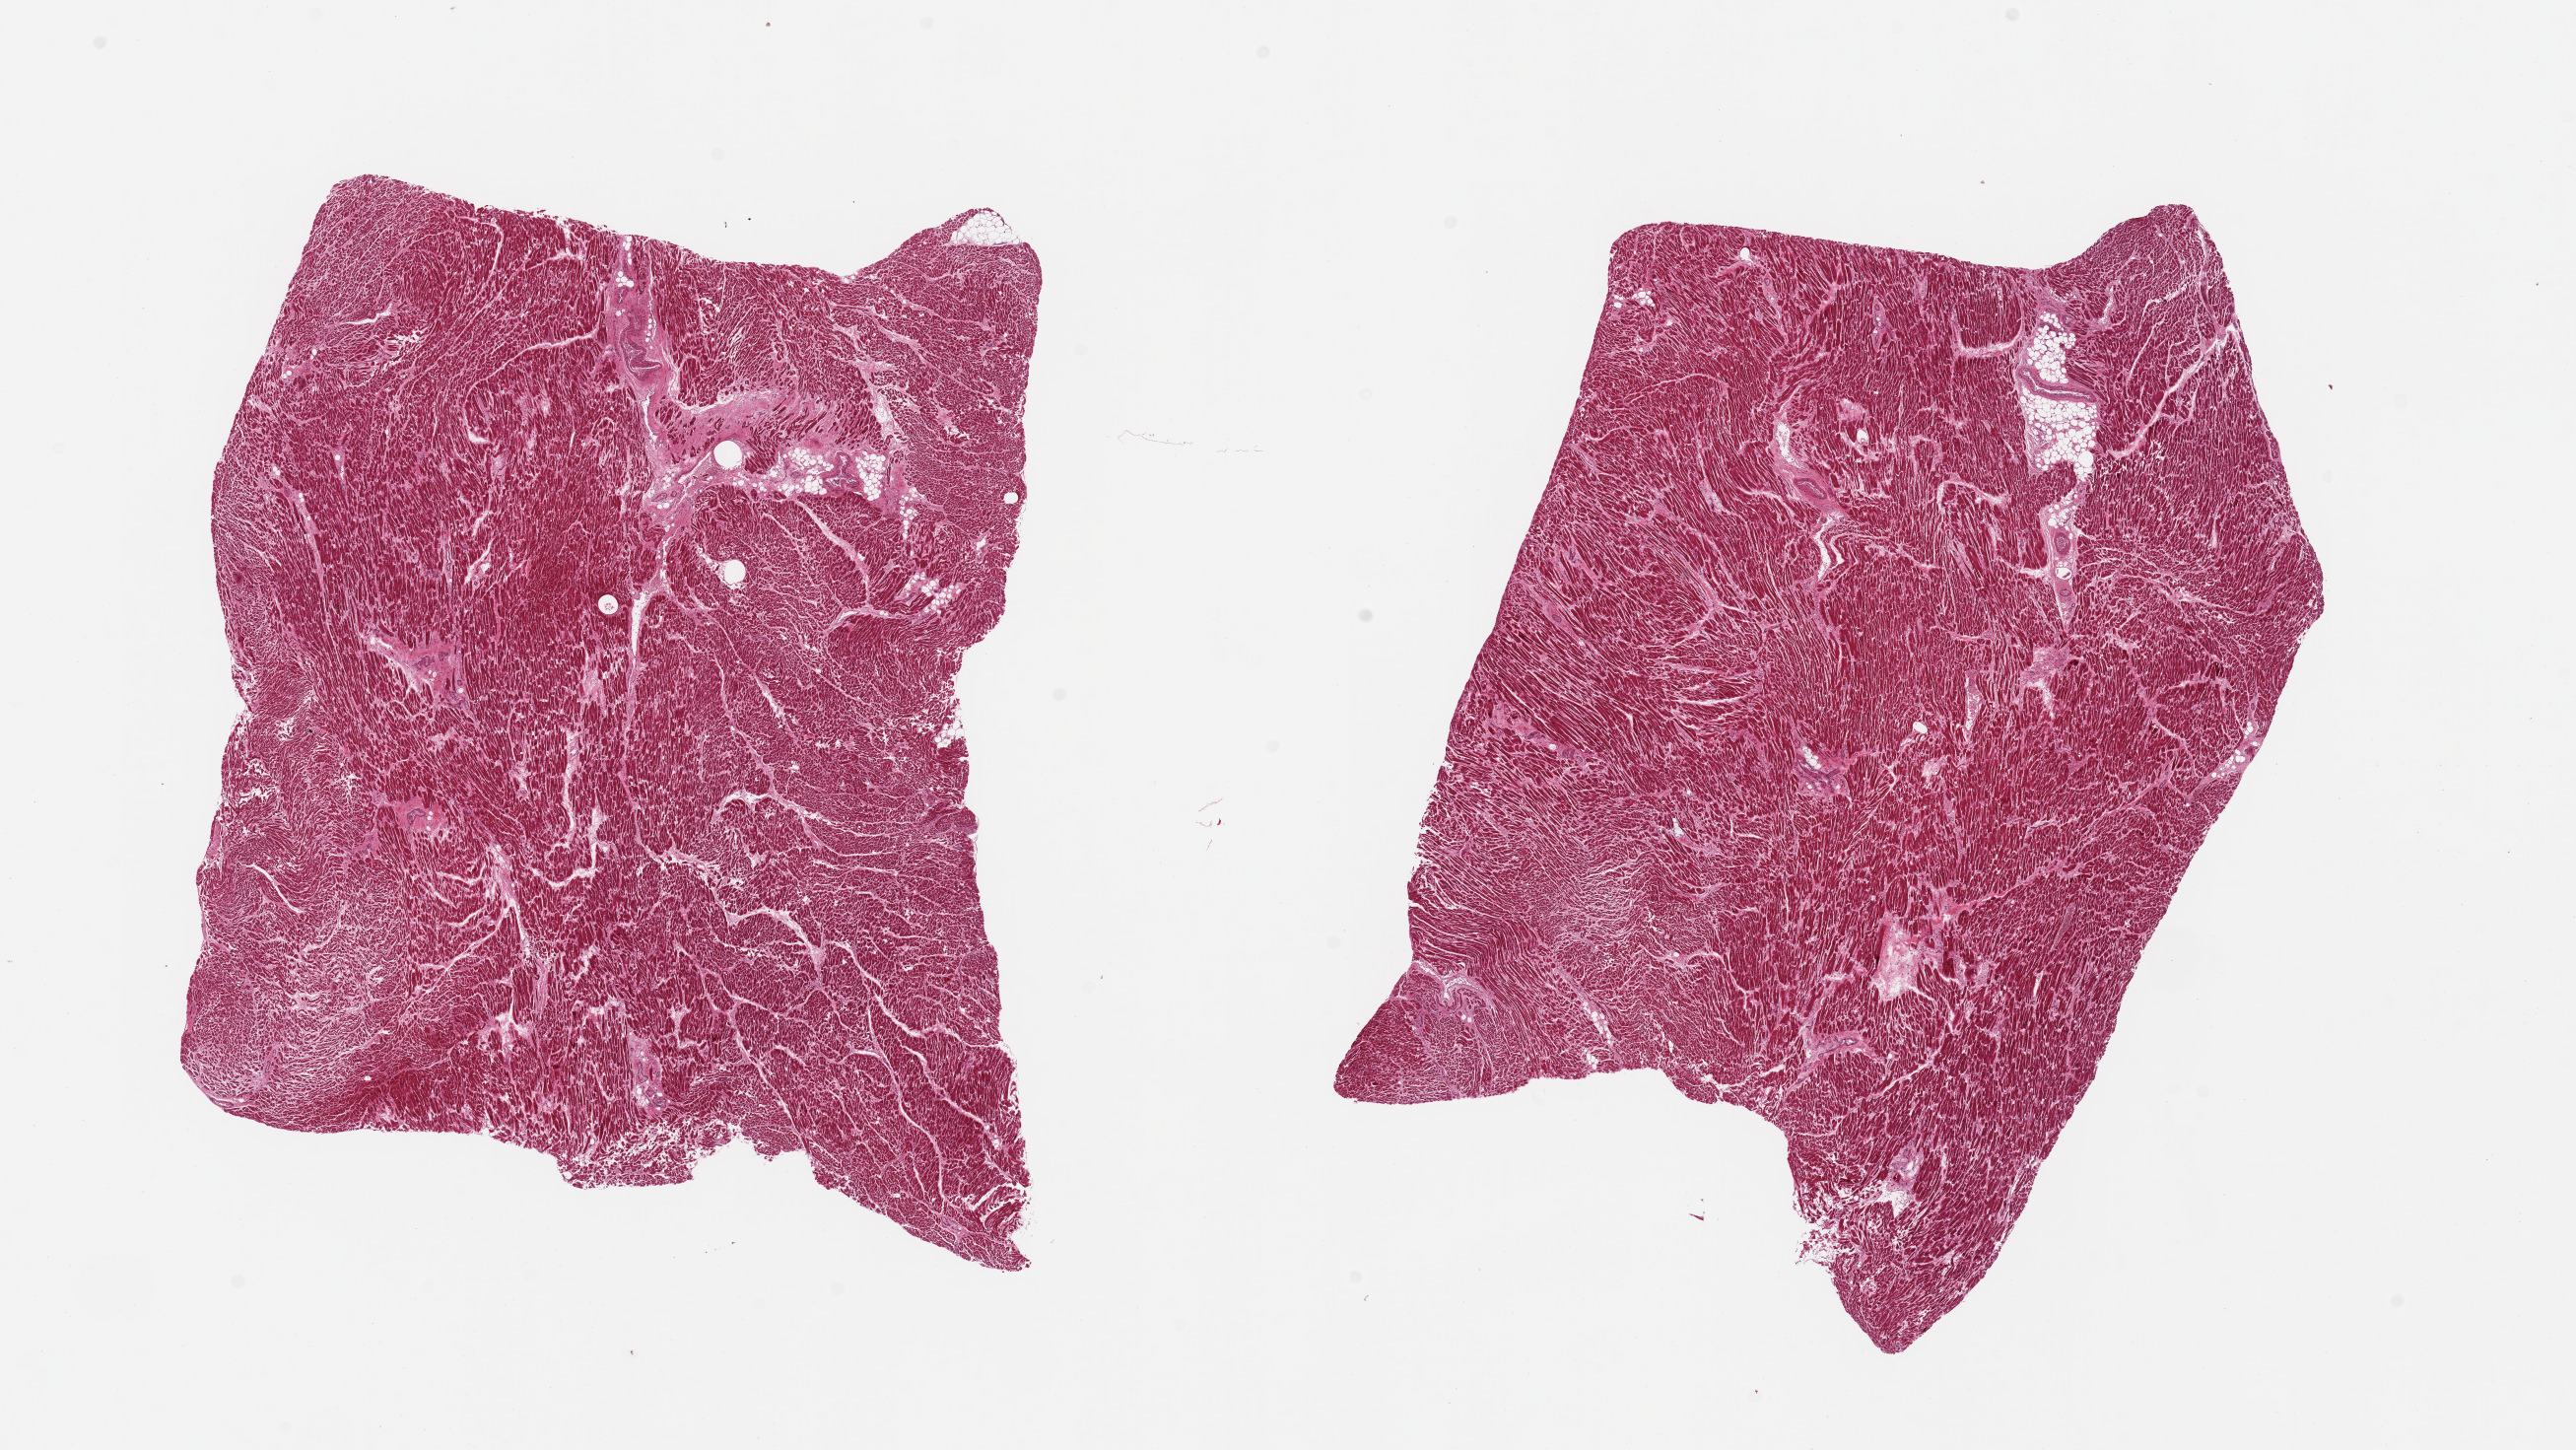
Hematoxylin and eosin (H&E) whole-slide image, brightfield — a low-resolution overview of the entire scanned area, about 20.7 x 11.6 mm, PAXgene-fixed paraffin-embedded (PFPE) section, section of heart (target tissue), tissue donor sample. Donor: male.
Pathologist's review note for this sample: 2 pieces, mild/moderate interstitial fibrosis; remote microinfarct (~2mm).